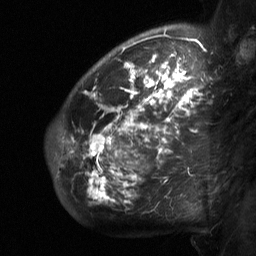
Breast MRI (dynamic contrast-enhanced), one sagittal slice. Slice 49 of 64 in the series (ordered by position). Dynamic contrast-enhanced study with each time point stored as its own series, time point 2 of 3 at this slice position (early post-contrast, ordered by acquisition time). 1.5 T. TE 4.8 ms, TR 27 ms. 2 mm slice thickness. 256 × 256 image matrix. Female patient, age 50 years. From the clinical record (not read from this slice): setting: breast cancer imaged before/during neoadjuvant chemotherapy; receptor status: HER2-positive.
Outlined on this slice (semi-automatic segmentation, software-assisted and operator-edited):
- analysis volume of interest (the breast-tissue region the enhancement analysis was run in; not a lesion): bounding box [x1, y1, x2, y2] px = [49, 62, 214, 214]
- tumour enhancement mask (voxels above the 90 % enhancement threshold inside the analysis volume of interest): [72, 62, 202, 202]